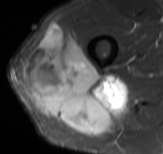
MRI of an extremity soft-tissue mass, one axial slice; position 50 of 61 along the scan axis; STIR; MR volume resampled by the dataset authors to the PET/CT grid (not the native acquisition matrix); 3.27 mm slice thickness; 163 × 154 image matrix. Male patient. From the clinical record (not read from this slice): histological type: poorly differentiated synovial sarcoma; grade: high; site of the primary tumour: right buttock.
Annotated regions visible in this slice (expert contour drawn on MRI and transferred to this co-registered scan by the dataset authors):
- gross tumour volume including surrounding oedema: bounding box [x1, y1, x2, y2] px = [23, 23, 127, 136]
- gross tumour volume (mass): [23, 23, 127, 136]